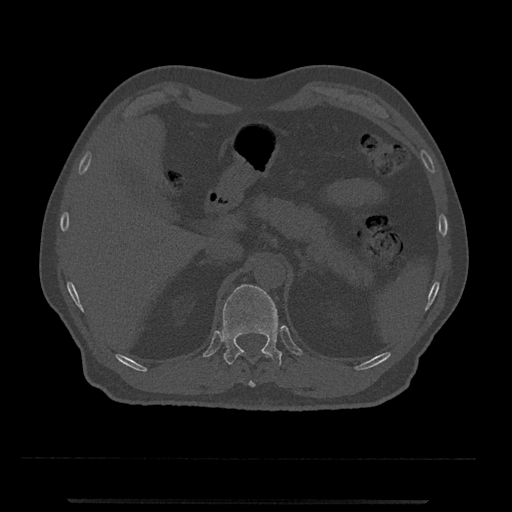
CT including the spine, one axial slice; 120 kVp; bone window (W 1800 / L 400 HU); 0.5 mm slice thickness; 512 × 512 image matrix, field of view 419 × 419 mm. Patient: male, 63 years. From the clinical record (not read from this slice): primary cancer: prostate.
Structures marked on this image (semi-automatic segmentation, software-assisted and operator-edited):
- T11 vertebra: bounding box [x1, y1, x2, y2] px = [236, 351, 270, 387]
- T12 vertebra: [223, 284, 283, 366]